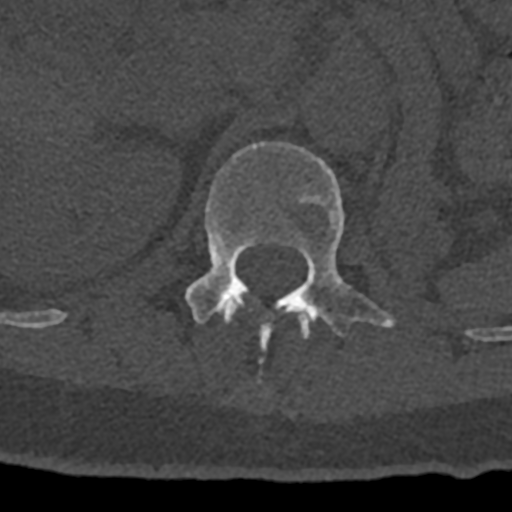
CT including the spine, one axial slice. Position 447 of 797 along the scan axis. Reconstruction kernel Br40s/3. 120 kVp. Bone window (W 1800 / L 400 HU). 0.5 mm slice thickness. 512 × 512 image matrix, field of view 160 × 160 mm. Male patient, age 74 years. Case-level facts recorded for this patient, not image findings: primary cancer: renal; vertebrae with lytic lesions (as recorded): T10, L1, L2, L3, L4, L5.
Outlined on this slice (semi-automatic segmentation, software-assisted and operator-edited):
- L1 vertebra: bounding box <185,142,395,382> (left, top, right, bottom; pixels)
- T12 vertebra: <220,297,315,339>